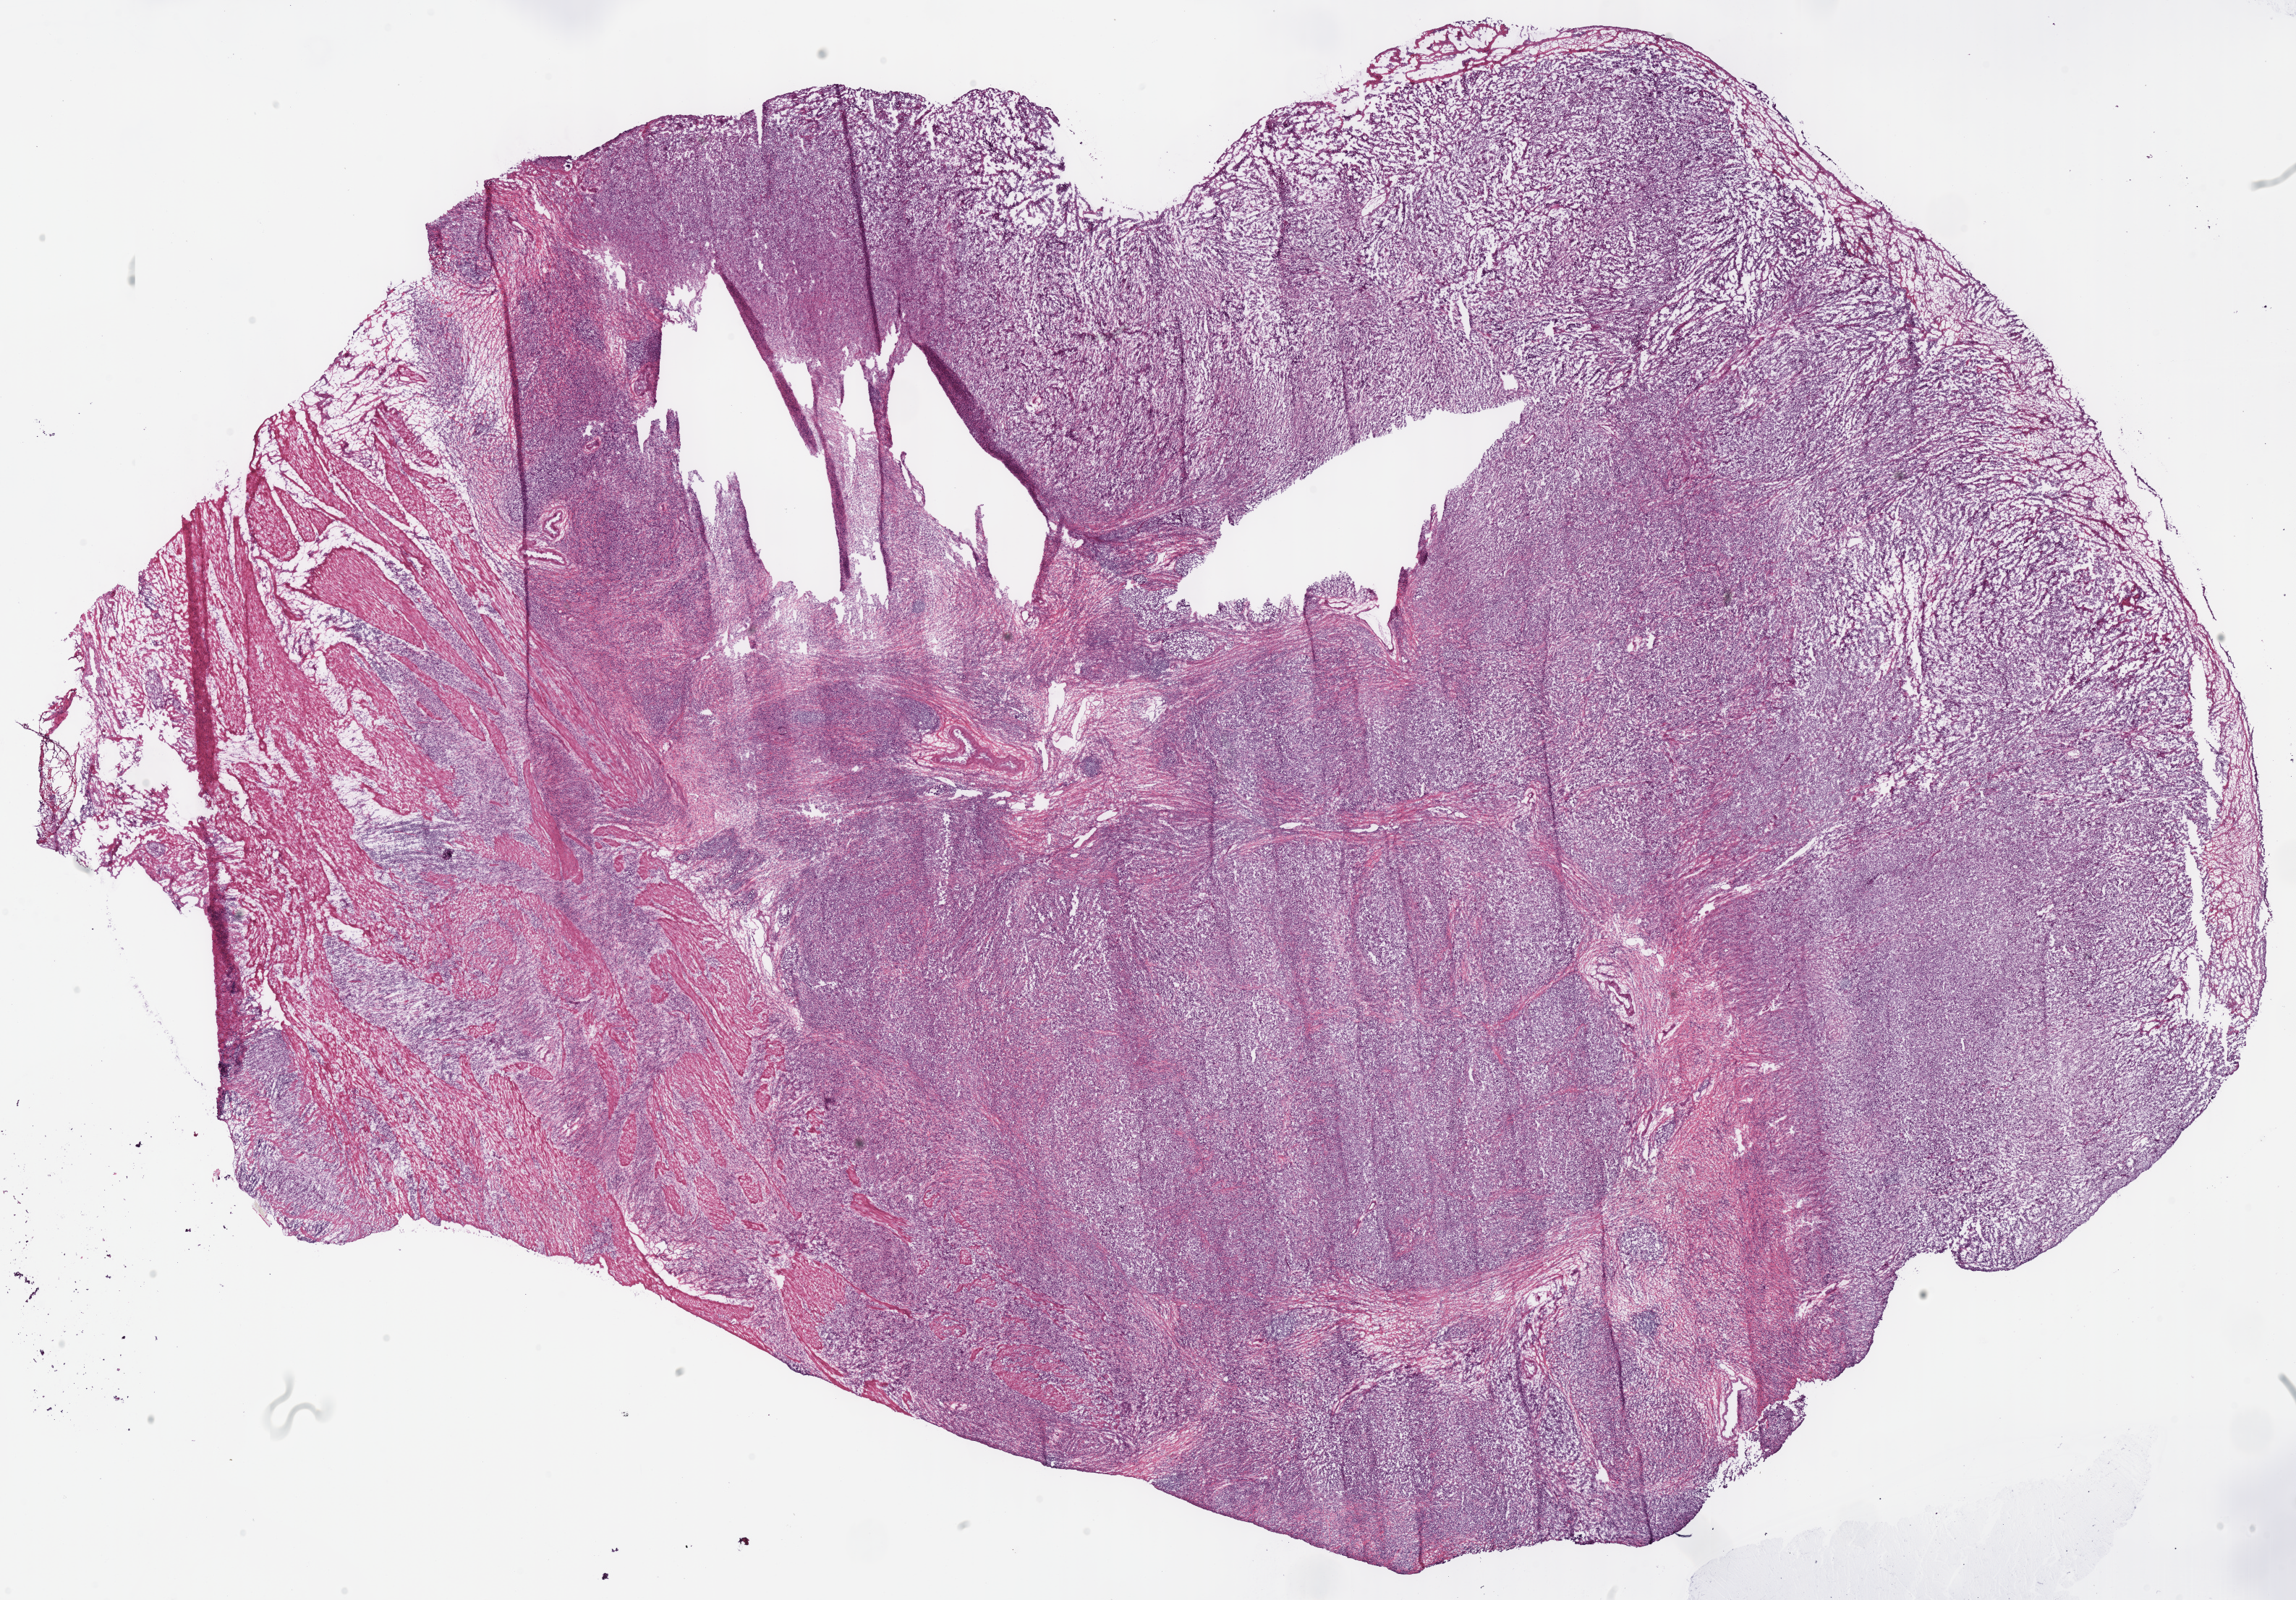
Hematoxylin and eosin (H&E) stained whole-slide image — whole scanned area (about 25.0 x 17.4 mm, slide scanned at 40x) shown as a low-resolution overview; frozen section from the bottom of the tissue portion; sample: primary tumour, stomach. Female, age 72 years at initial diagnosis. Histologic grade: G3 (poorly differentiated). Composition of this section per pathologist review: tumour cells 80%, tumour nuclei 75%, normal cells 0%, stromal cells 20%, necrosis 0%.
TNM: T4a N3a M0. AJCC pathologic stage: IIIC (7th edition). Histologic diagnosis: Adenocarcinoma, intestinal type (gastric antrum). Lymph nodes positive (case pathology): 9 of 9 examined.